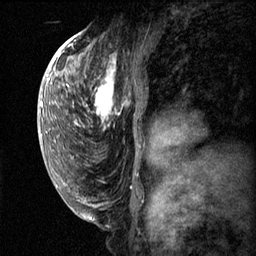
Breast MRI (dynamic contrast-enhanced), one sagittal slice. Slice 34 of 60 in the series (ordered by position). Dynamic contrast-enhanced series, image 2 of 3 at this slice position (ordered by acquisition). 1.5 T. TE 4.2 ms, TR 11.1 ms. 2 mm slice thickness. 256 × 256 image matrix, field of view 180 × 180 mm. Female patient, age 50 years.
Outlined on this slice (semi-automatic segmentation, software-assisted and operator-edited):
- analysis volume of interest (the breast-tissue region the enhancement analysis was run in; not a lesion): bounding box (x1, y1, x2, y2) in pixels: (82, 56, 161, 143)
- tumour enhancement mask (voxels above the 70 % enhancement threshold inside the analysis volume of interest): (83, 62, 116, 129)